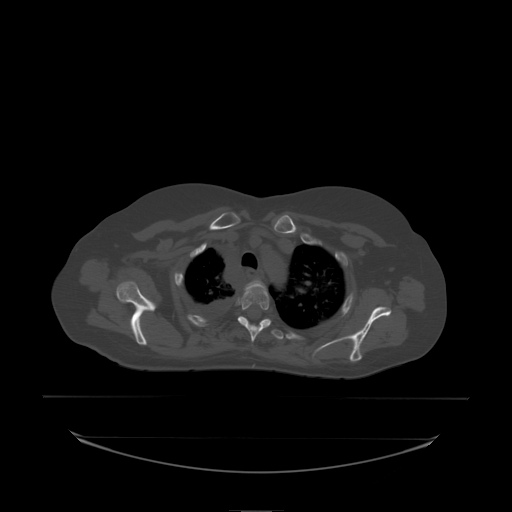
CT including the spine, one axial slice. Position 173 of 242 along the scan axis. Bone window (W 1800 / L 400 HU). 2.5 mm slice thickness. 512 × 512 image matrix, field of view 500 × 500 mm. Patient: female, 53 years. Case-level facts recorded for this patient, not image findings: primary cancer: lung; vertebrae with lytic lesions (as recorded): T7, L1.
Annotated regions visible in this slice (semi-automatic segmentation, software-assisted and operator-edited):
- T2 vertebra: box from (x=245, y=280) to (x=265, y=289) px
- T3 vertebra: (x=238, y=284)–(x=271, y=338)
- T4 vertebra: (x=238, y=316)–(x=283, y=336)